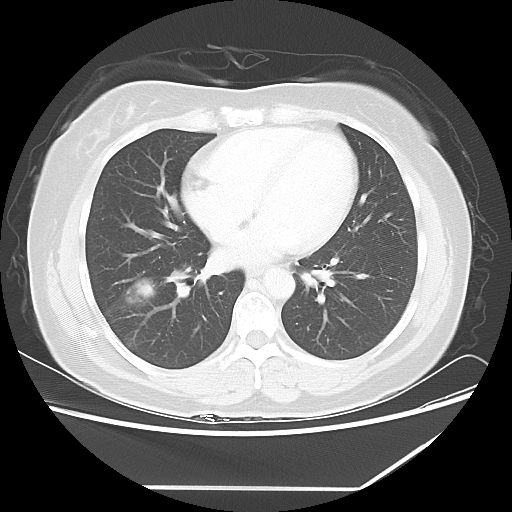
Chest CT, one axial slice; slice 27 of 60 in the series (ordered by position); 100 kVp; lung window (W 1500 / L -600 HU); 512 × 512 image matrix, field of view 374 × 374 mm. Patient: female, 42 years. Case-level facts recorded for this patient, not image findings: clinical TNM (as recorded): T2 N1 M0.
Structures marked on this image (bounding box drawn by a radiologist):
- lung tumour (recorded histology: adenocarcinoma): bounding box <119,271,160,309> (left, top, right, bottom; pixels)